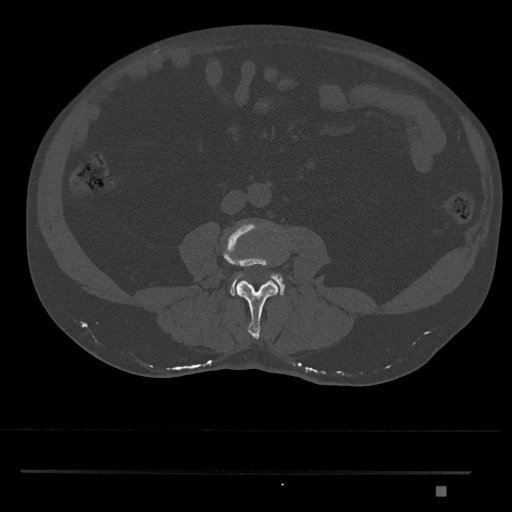
CT including the spine, one axial slice; position 659 of 1134 along the scan axis; reconstruction kernel Br40s/3; bone window (W 1800 / L 400 HU); 0.5 mm slice thickness; 512 × 512 image matrix, field of view 429 × 429 mm. Male patient, age 65 years. Case-level facts recorded for this patient, not image findings: primary cancer: prostate.
Annotated regions visible in this slice (semi-automatically segmented with operator editing):
- L3 vertebra: bounding box [x1, y1, x2, y2] px = [221, 220, 284, 339]
- L4 vertebra: [230, 273, 285, 296]